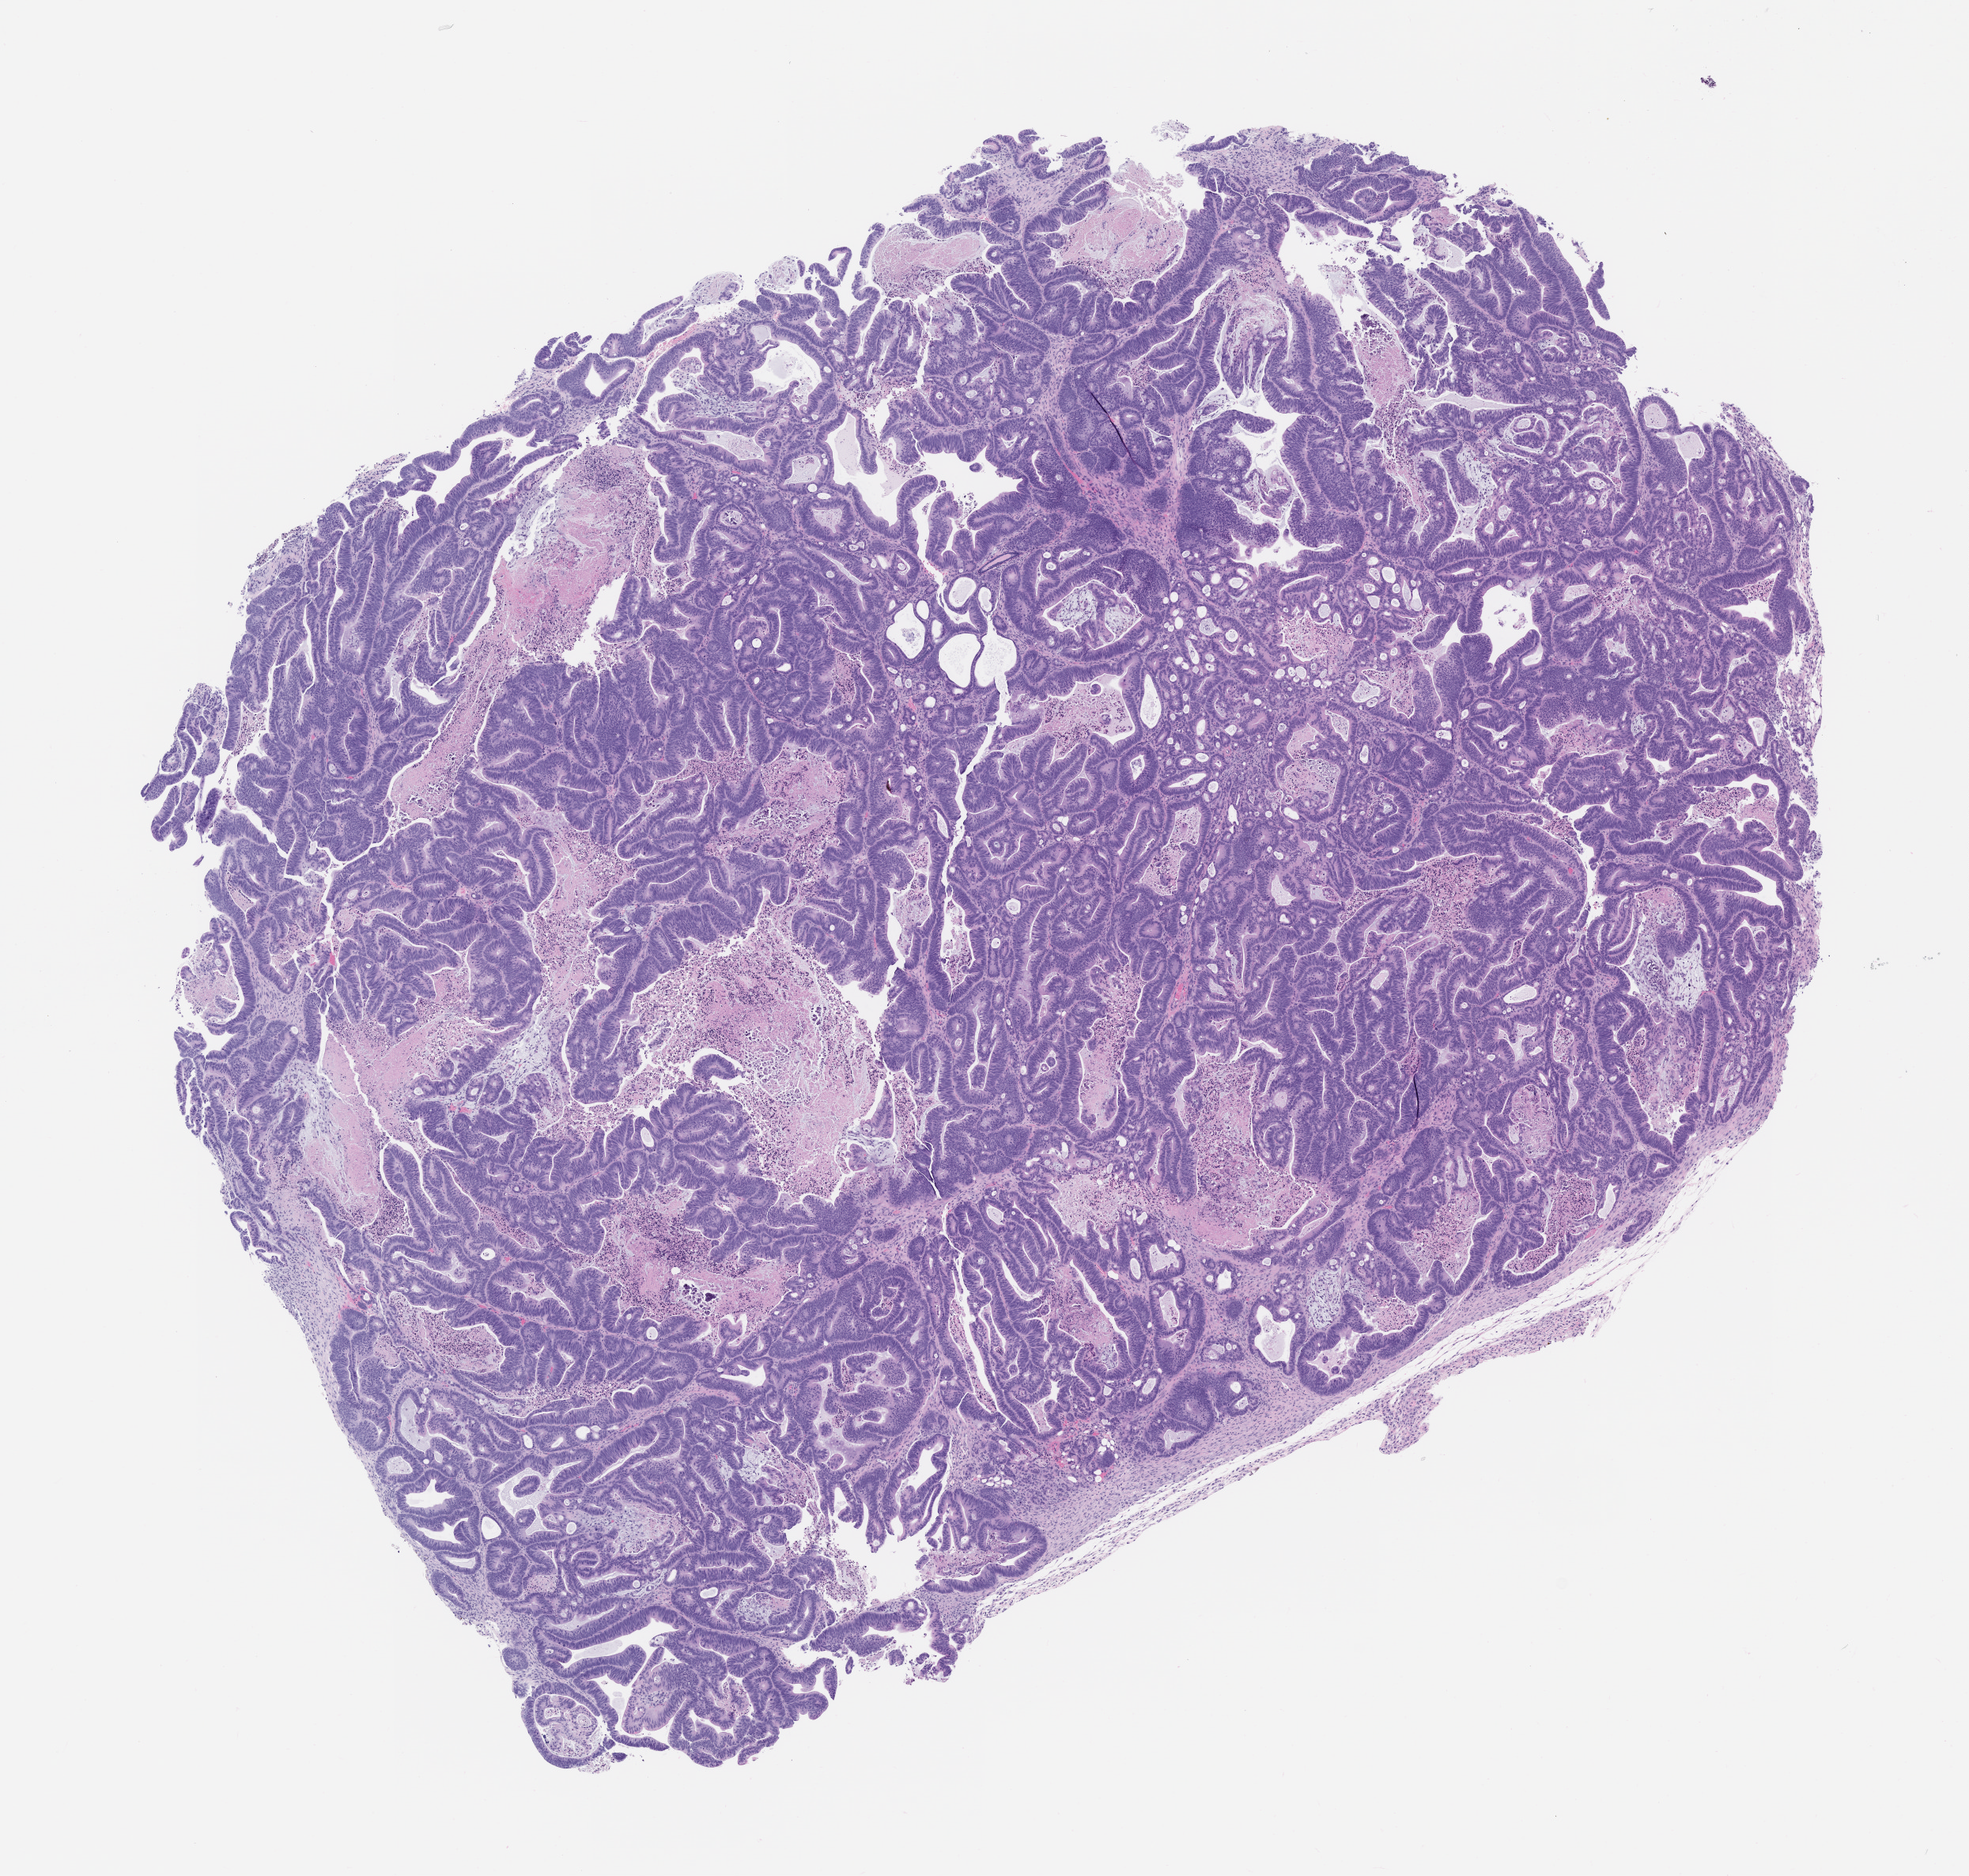
Whole-slide image, hematoxylin and eosin (H&E): patient-derived xenograft (human tumor grown in a mouse), passage 2, a low-resolution overview of the entire scanned area, about 10.0 x 9.5 mm. FFPE section. Originating tumor site category: colon.
• originating patient diagnosis: Colon Adenocarcinoma